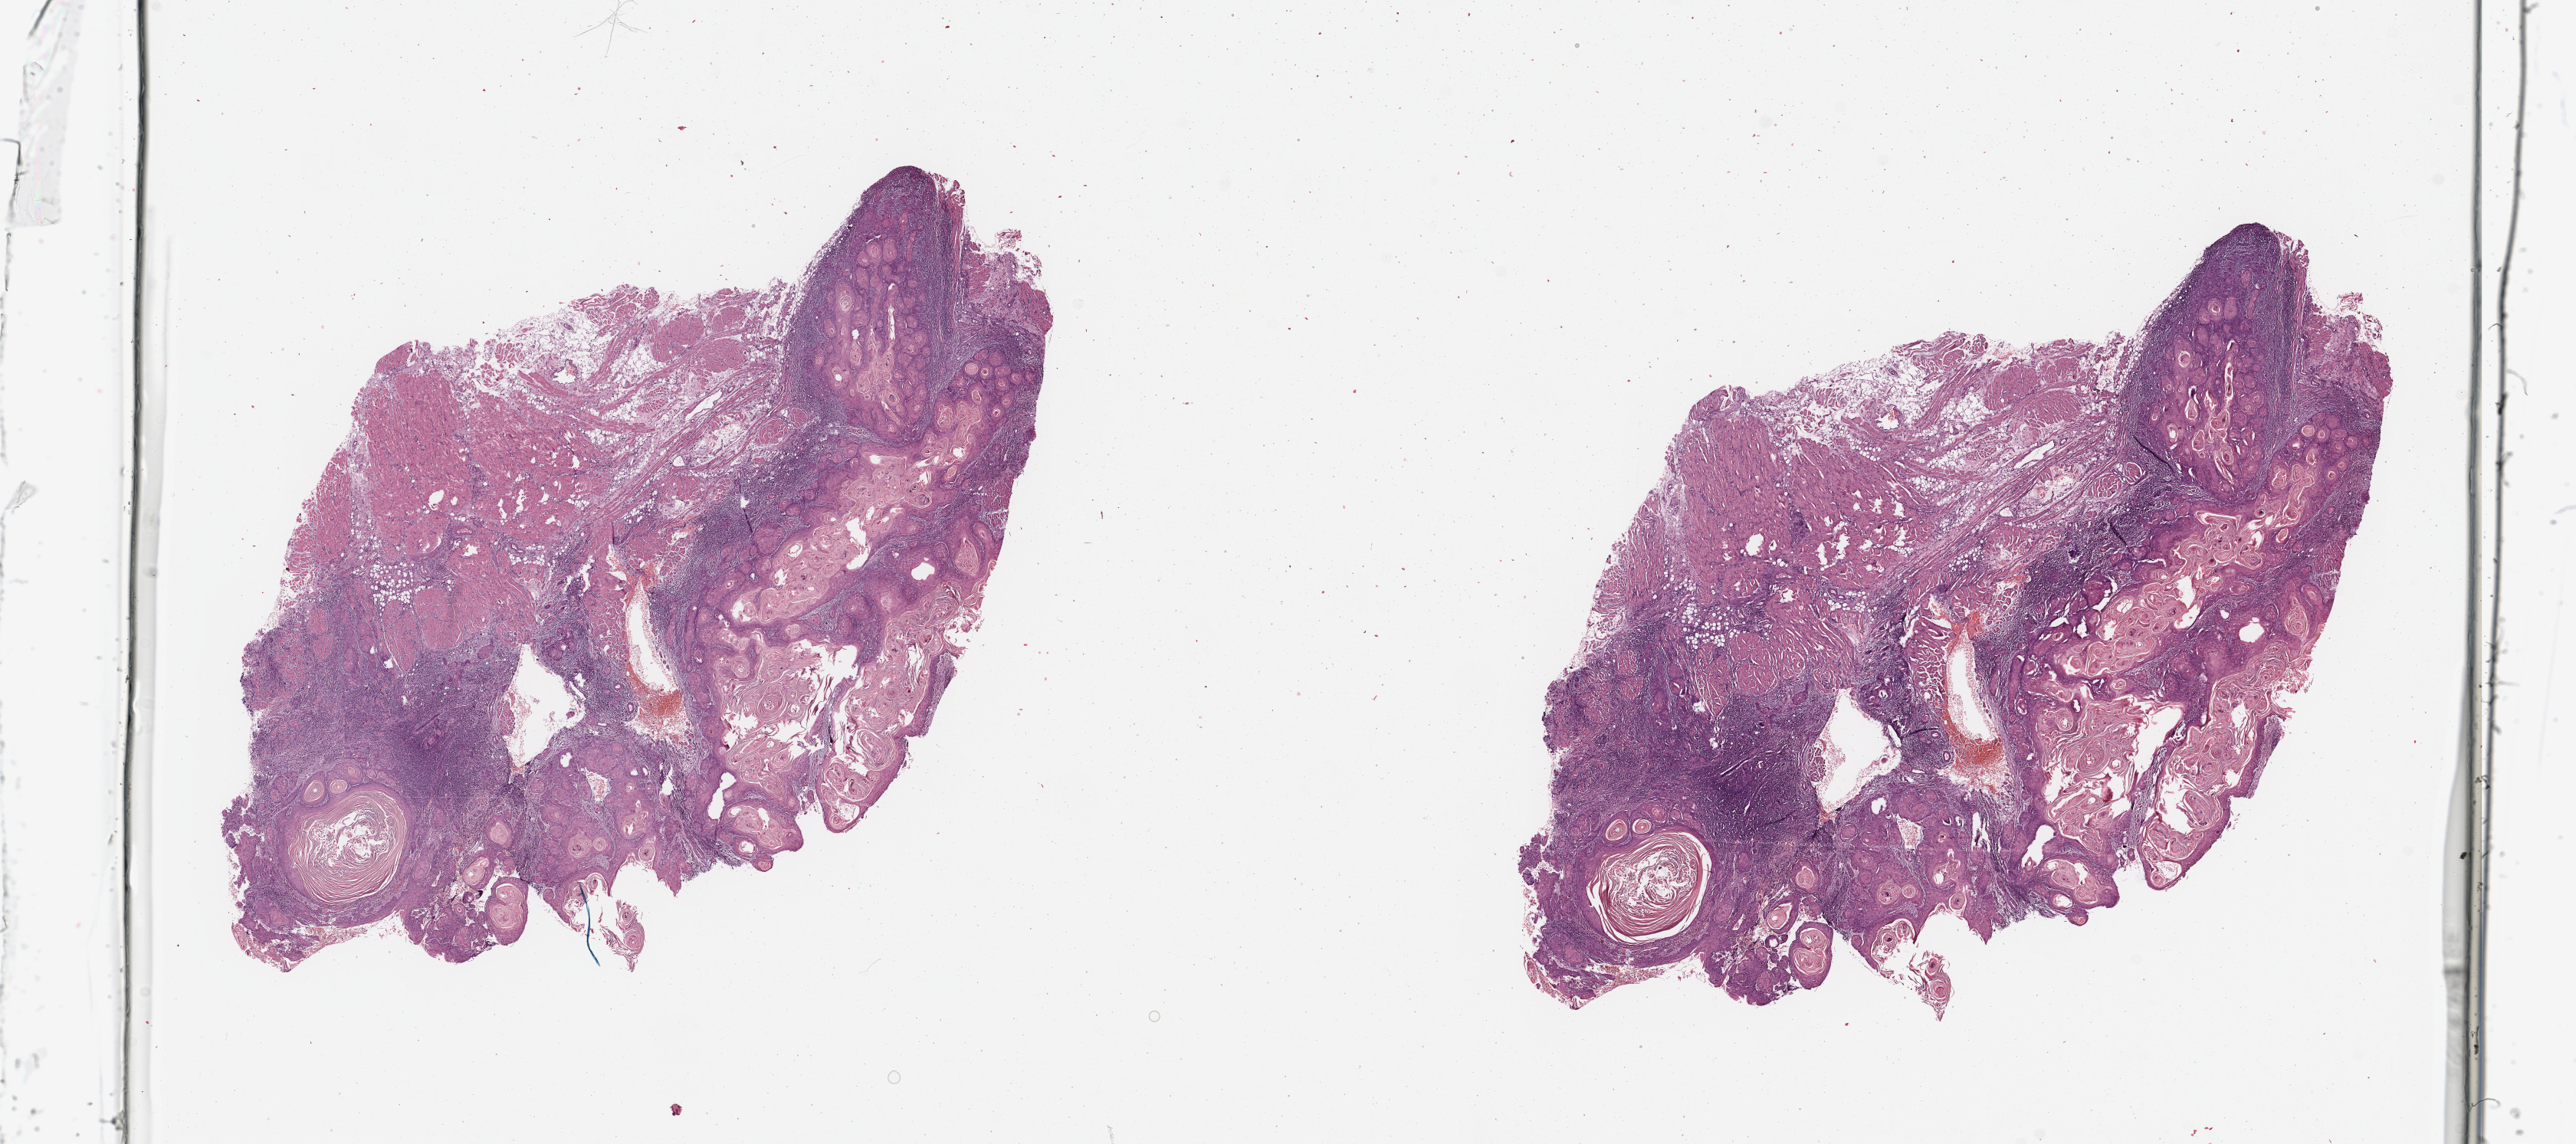
Whole-slide histology image, H&E-stained — low-resolution overview of the scanned area, about 26.6 x 11.8 mm (slide scanned at 20x); head and neck, tissue type not recorded. 60-year-old female patient.
Patient diagnosis: Squamous cell carcinoma, NOS (tongue, NOS).